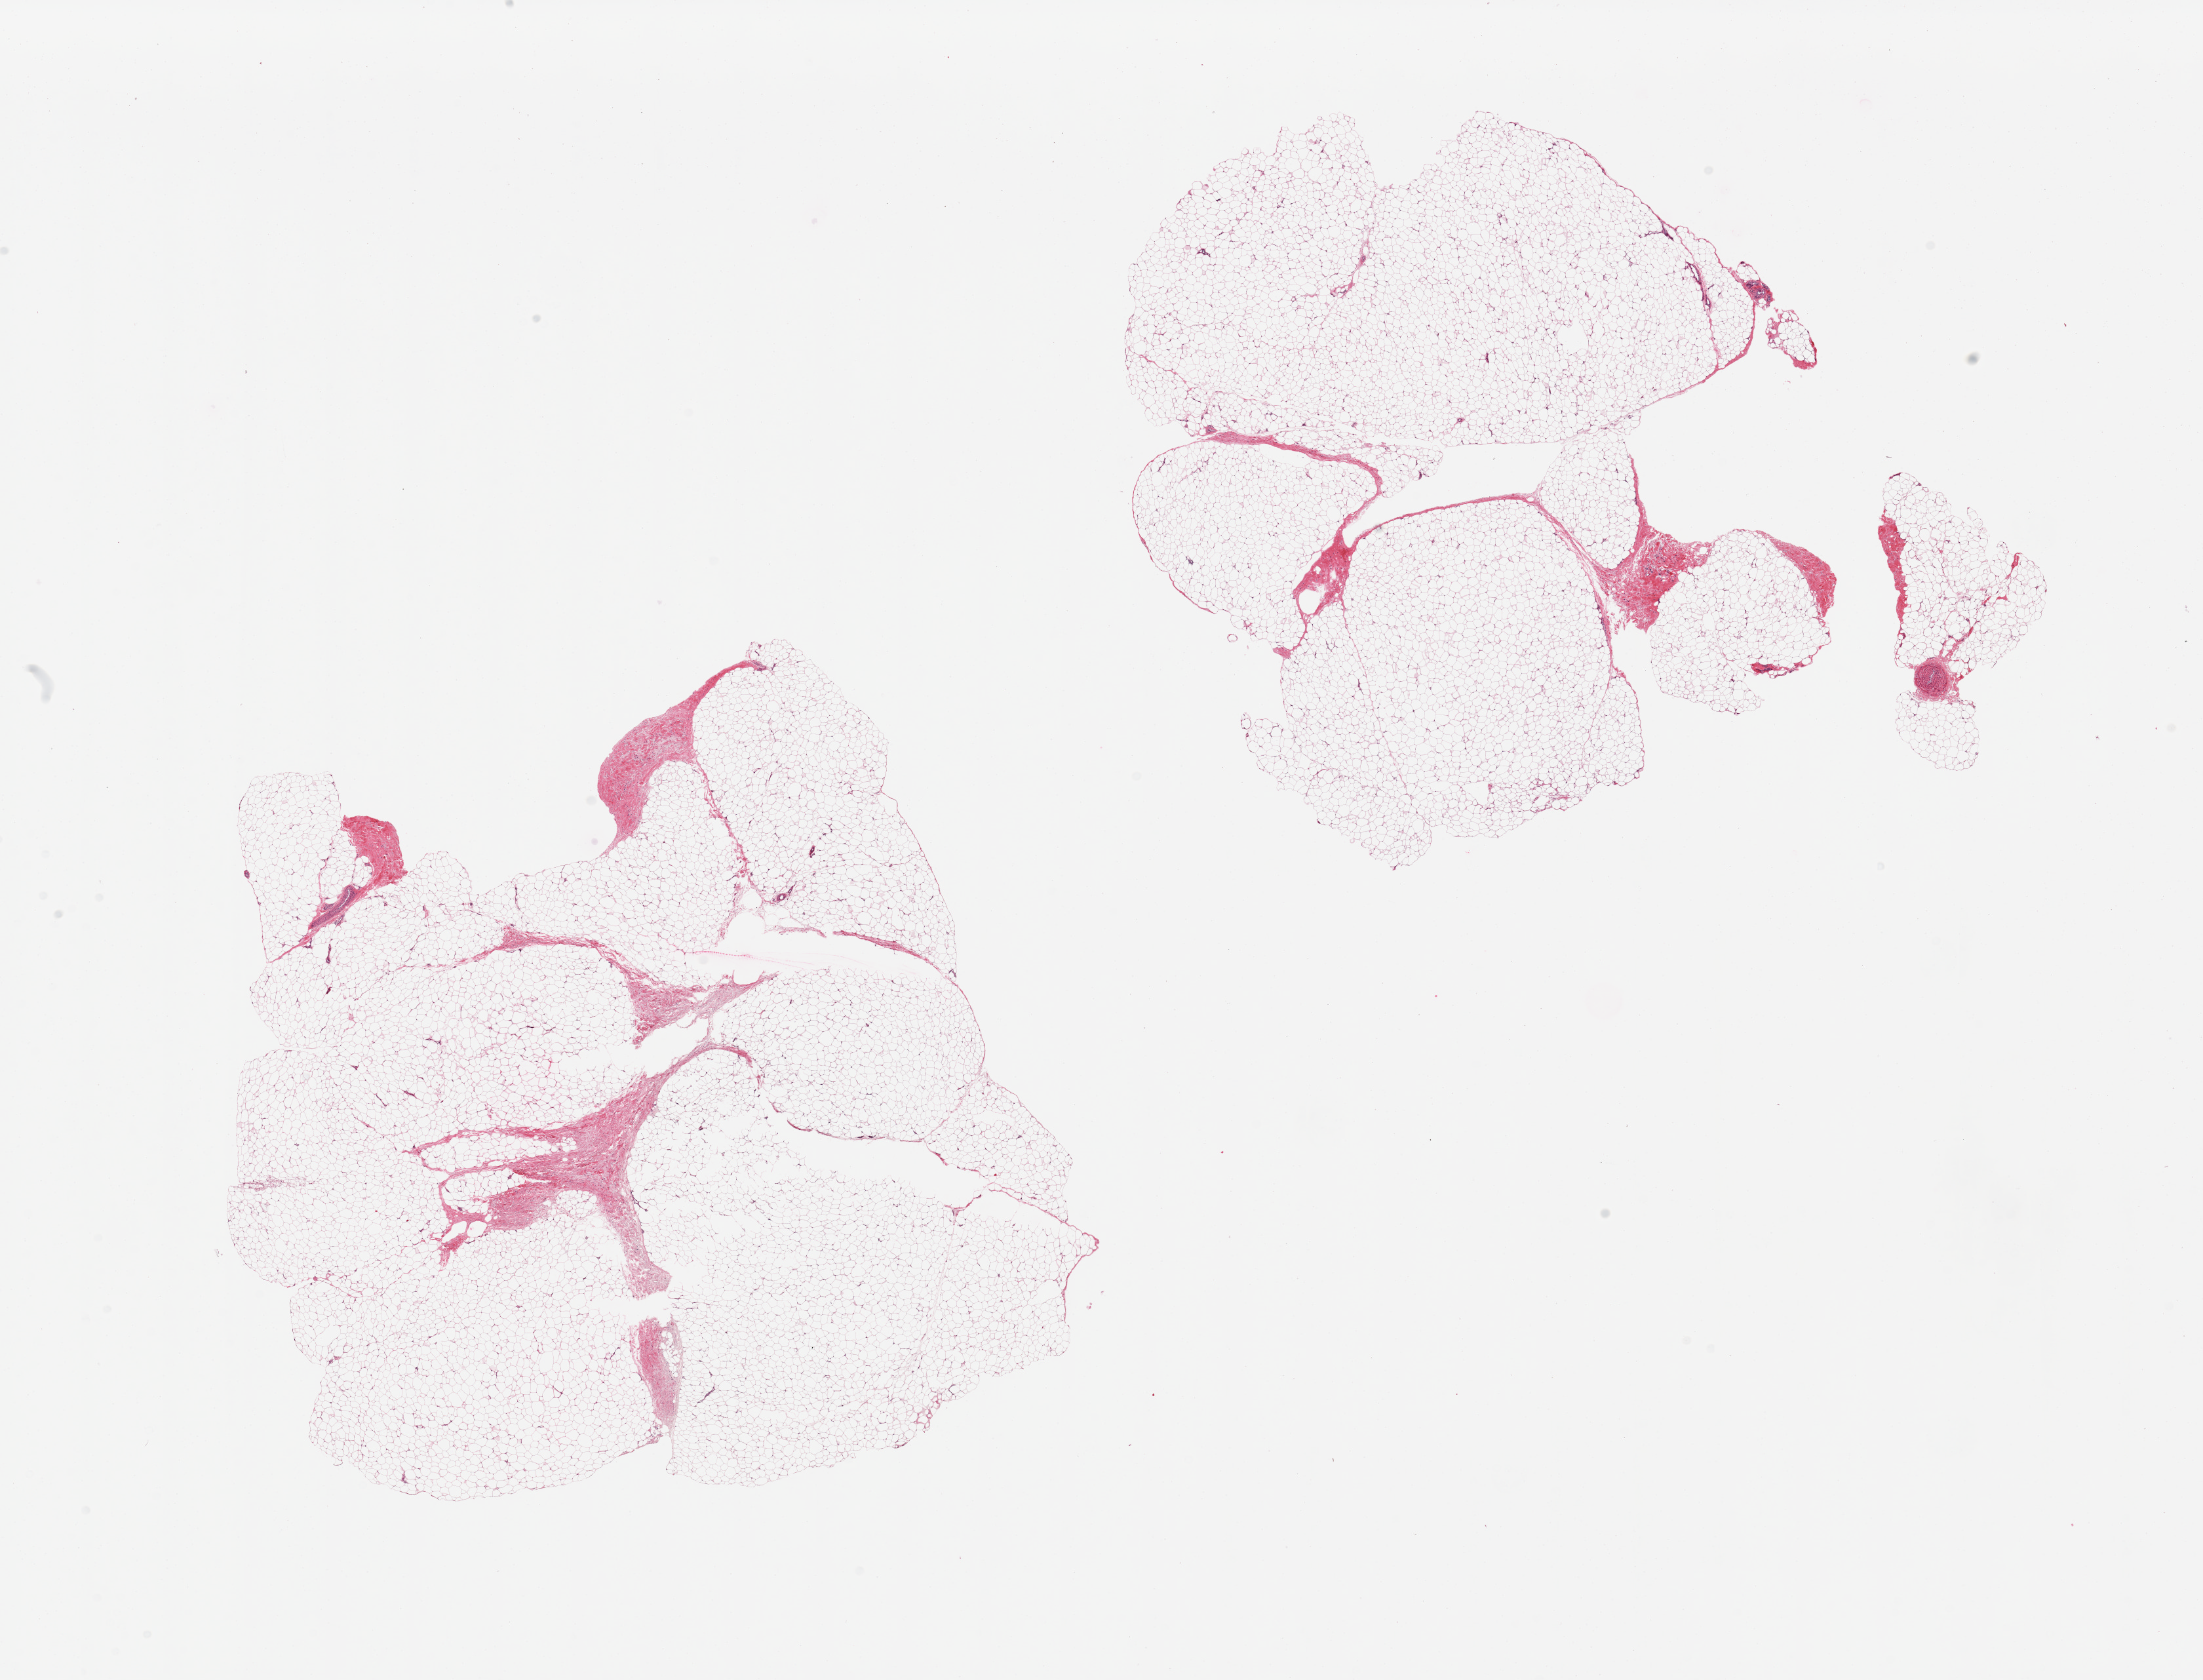
Digitized hematoxylin and eosin (H&E)-stained section, a low-resolution overview of the entire scanned area, about 26.6 x 20.3 mm. PAXgene-fixed, paraffin-embedded tissue. Sampled site (target tissue): adipose tissue. Donor tissue sample. Donor sex: female.
Pathologist's review note for this sample: 2 pieces, ~10-15% fibrous tissue.